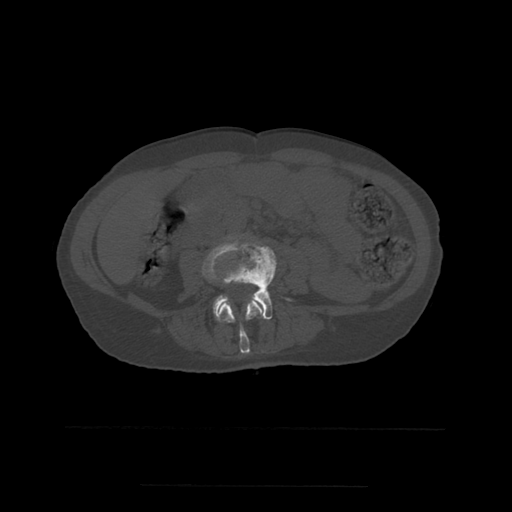
CT including the spine, one axial slice; bone window (W 1800 / L 400 HU); 1.25 mm slice thickness; 512 × 512 image matrix. Patient age 58 years. From the clinical record (not read from this slice): primary cancer: lung.
Annotated regions visible in this slice (semi-automatically segmented with operator editing):
- L3 vertebra: box from (x=201, y=240) to (x=264, y=354) px
- L4 vertebra: (x=213, y=243)–(x=290, y=320)